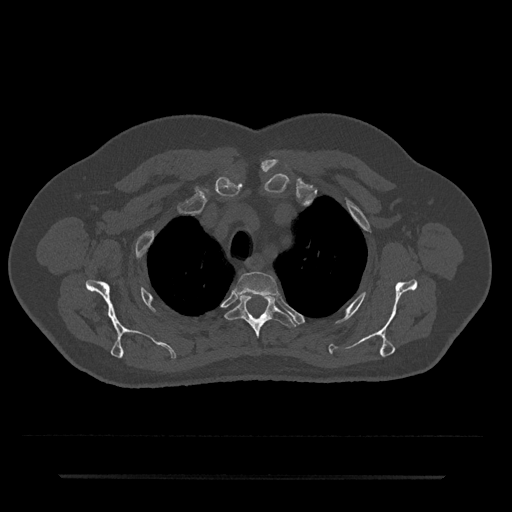
CT including the spine, one axial slice. Position 577 of 797 along the scan axis. Bone window (W 1800 / L 400 HU). 512 × 512 image matrix, field of view 437 × 437 mm. Male patient, age 69 years. Case-level facts recorded for this patient, not image findings: primary cancer: prostate.
Annotated regions visible in this slice (semi-automatic segmentation, software-assisted and operator-edited):
- T2 vertebra: bounding box [x1, y1, x2, y2] px = [235, 272, 278, 295]
- T3 vertebra: [225, 295, 297, 338]